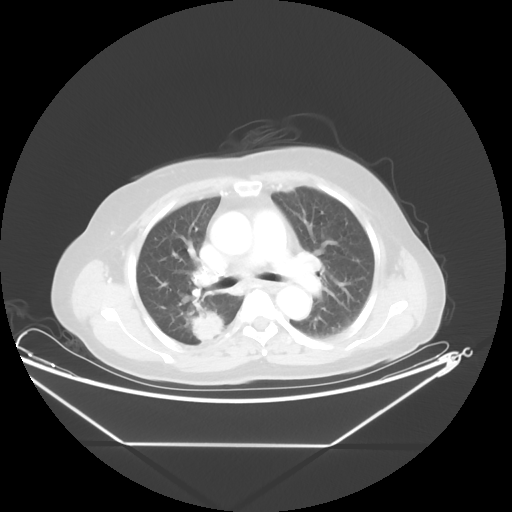
Chest CT, one axial slice. Position 29 of 48 along the scan axis. Reconstruction kernel STANDARD. Lung window (W 1500 / L -600 HU). 5 mm slice thickness. 512 × 512 image matrix, field of view 462 × 462 mm. Patient: female, 62 years. From the clinical record (not read from this slice): clinical TNM (as recorded): T1c N0 M0; histopathological grade: G2-3.
Outlined on this slice (rectangle marked by the reading radiologist):
- lung tumour (recorded histology: adenocarcinoma): bounding box [x1, y1, x2, y2] px = [187, 305, 232, 353]